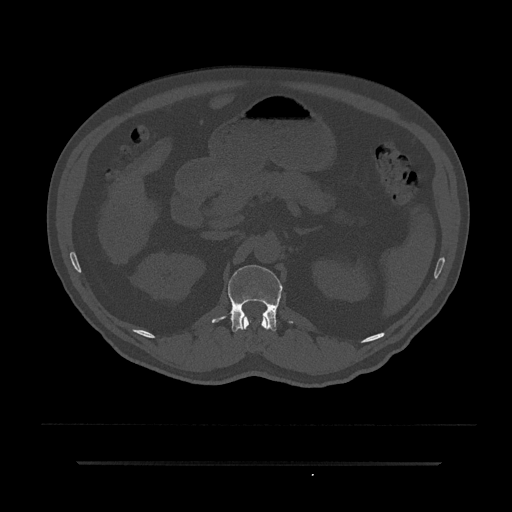
CT including the spine, one axial slice. Reconstruction kernel Br40s/3. Bone window (W 1800 / L 400 HU). 0.5 mm slice thickness. 512 × 512 image matrix, field of view 464 × 464 mm. Male patient, age 59 years. Case-level facts recorded for this patient, not image findings: primary cancer: bile ducts; vertebrae with lytic lesions (as recorded): T10.
Outlined on this slice (semi-automatically segmented with operator editing):
- L1 vertebra: box from (x=212, y=265) to (x=292, y=333) px
- T12 vertebra: (x=240, y=316)–(x=268, y=330)